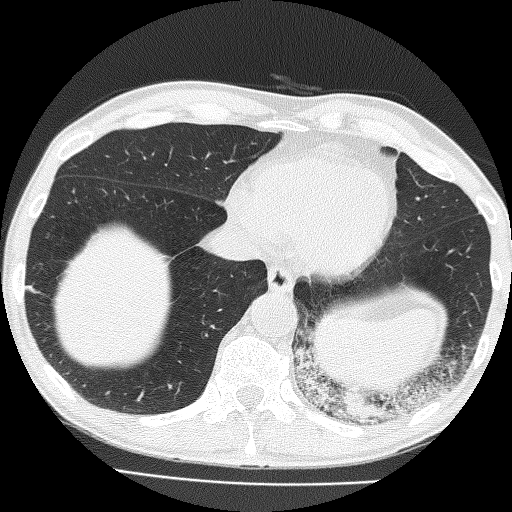
Low-dose screening chest CT, one axial slice. Position 47 of 160 along the scan axis. 120 kVp. Lung window (W 1500 / L -600 HU). 512 × 512 image matrix, field of view 324 × 324 mm.
Outlined on this slice (expert manual segmentation):
- lesion 1 (tumor, lower lobe of left lung): bounding box [x1, y1, x2, y2] px = [342, 391, 387, 424]